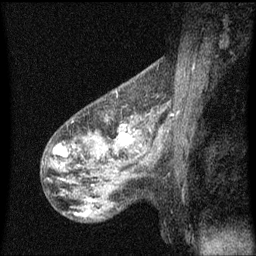
Breast MRI (dynamic contrast-enhanced), one sagittal slice. Slice 39 of 60 in the series (ordered by position). Dynamic contrast-enhanced series, image 2 of 3 at this slice position (ordered by acquisition). 1.5 T. TE 4.2 ms, TR 8 ms. 2 mm slice thickness. 256 × 256 image matrix. Female patient, age 50 years.
Outlined on this slice (semi-automatically segmented with operator editing):
- analysis volume of interest (the breast-tissue region the enhancement analysis was run in; not a lesion): bounding box (x1, y1, x2, y2) in pixels: (106, 118, 148, 159)
- tumour enhancement mask (voxels above the 70 % enhancement threshold inside the analysis volume of interest): (120, 124, 134, 143)